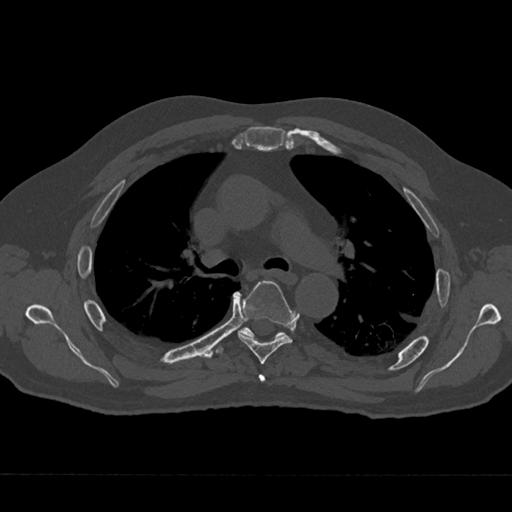
CT including the spine, one axial slice. Slice 461 of 797 in the series (ordered by position). 120 kVp. Bone window (W 1800 / L 400 HU). 0.5 mm slice thickness. 512 × 512 image matrix, field of view 377 × 377 mm. Male patient, age 75 years. Case-level facts recorded for this patient, not image findings: primary cancer: renal; vertebrae with lytic lesions (as recorded): T4.
Annotated regions visible in this slice (semi-automatically segmented with operator editing):
- T4 vertebra: bounding box <258,374,265,382> (left, top, right, bottom; pixels)
- T5 vertebra: <238,281,294,365>
- T6 vertebra: <238,327,284,339>